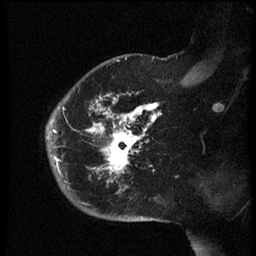
Breast MRI (dynamic contrast-enhanced), one sagittal slice. Slice 45 of 60 in the series (ordered by position). Dynamic contrast-enhanced series, image 2 of 3 at this slice position (ordered by acquisition). 1.5 T. TE 4.2 ms, TR 8.4 ms. 256 × 256 image matrix. Patient: female, 38 years. Case-level facts recorded for this patient, not image findings: setting: breast cancer imaged before/during neoadjuvant chemotherapy; receptor status: HER2-positive.
Structures marked on this image (semi-automatically segmented with operator editing):
- analysis volume of interest (the breast-tissue region the enhancement analysis was run in; not a lesion): bounding box (x1, y1, x2, y2) in pixels: (47, 74, 165, 202)
- tumour enhancement mask (voxels above the 70 % enhancement threshold inside the analysis volume of interest): (47, 94, 159, 176)